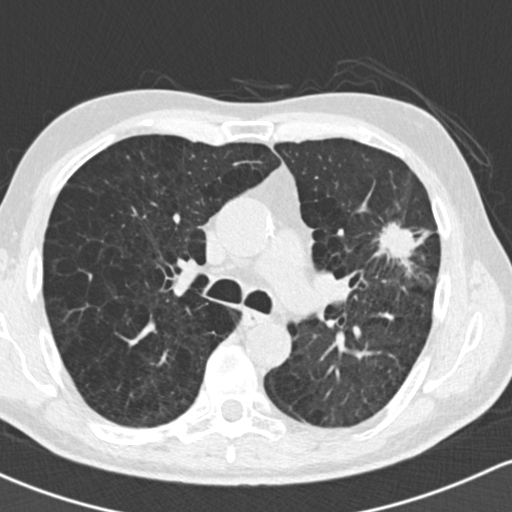
Low-dose screening chest CT, axial slice; first (baseline) screen; lung window (W 1500 / L -600 HU); standard (soft-tissue) reconstruction kernel (B30f); slice 66 of 162 in the series; 512 × 512 image matrix. Male participant, aged 61 years at enrolment. Former smoker at enrolment.
Lesion marked by an expert reader, bounding box <357,187,457,296> (left, top, right, bottom; pixels). The exam's reader record, not a measurement of the box and not confirmed to be the same lesion: non-calcified nodule or mass ≥4 mm, left upper lobe, 35 × 35 mm, spiculated (stellate) margins, soft tissue attenuation. Participant outcome: lung cancer diagnosed 19 days after this screen — adenocarcinoma, NOS, left upper lobe, well differentiated (G1), stage IIIA (AJCC 6th edition), 45 mm at pathology.